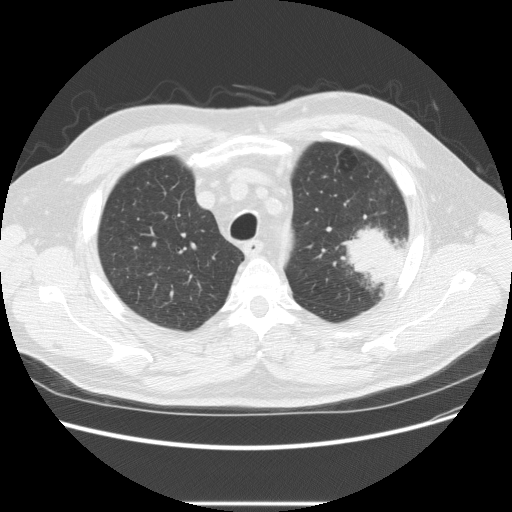
Low-dose screening chest CT, one axial slice. Slice 181 of 233 in the series (ordered by position). Reconstruction kernel STANDARD. 120 kVp. Lung window (W 1500 / L -600 HU). 2.5 mm slice thickness. 512 × 512 image matrix, field of view 380 × 380 mm.
Structures marked on this image (outlined manually by an expert reader):
- lesion 1 (tumor, upper lobe of left lung): box from (x=341, y=226) to (x=401, y=291) px